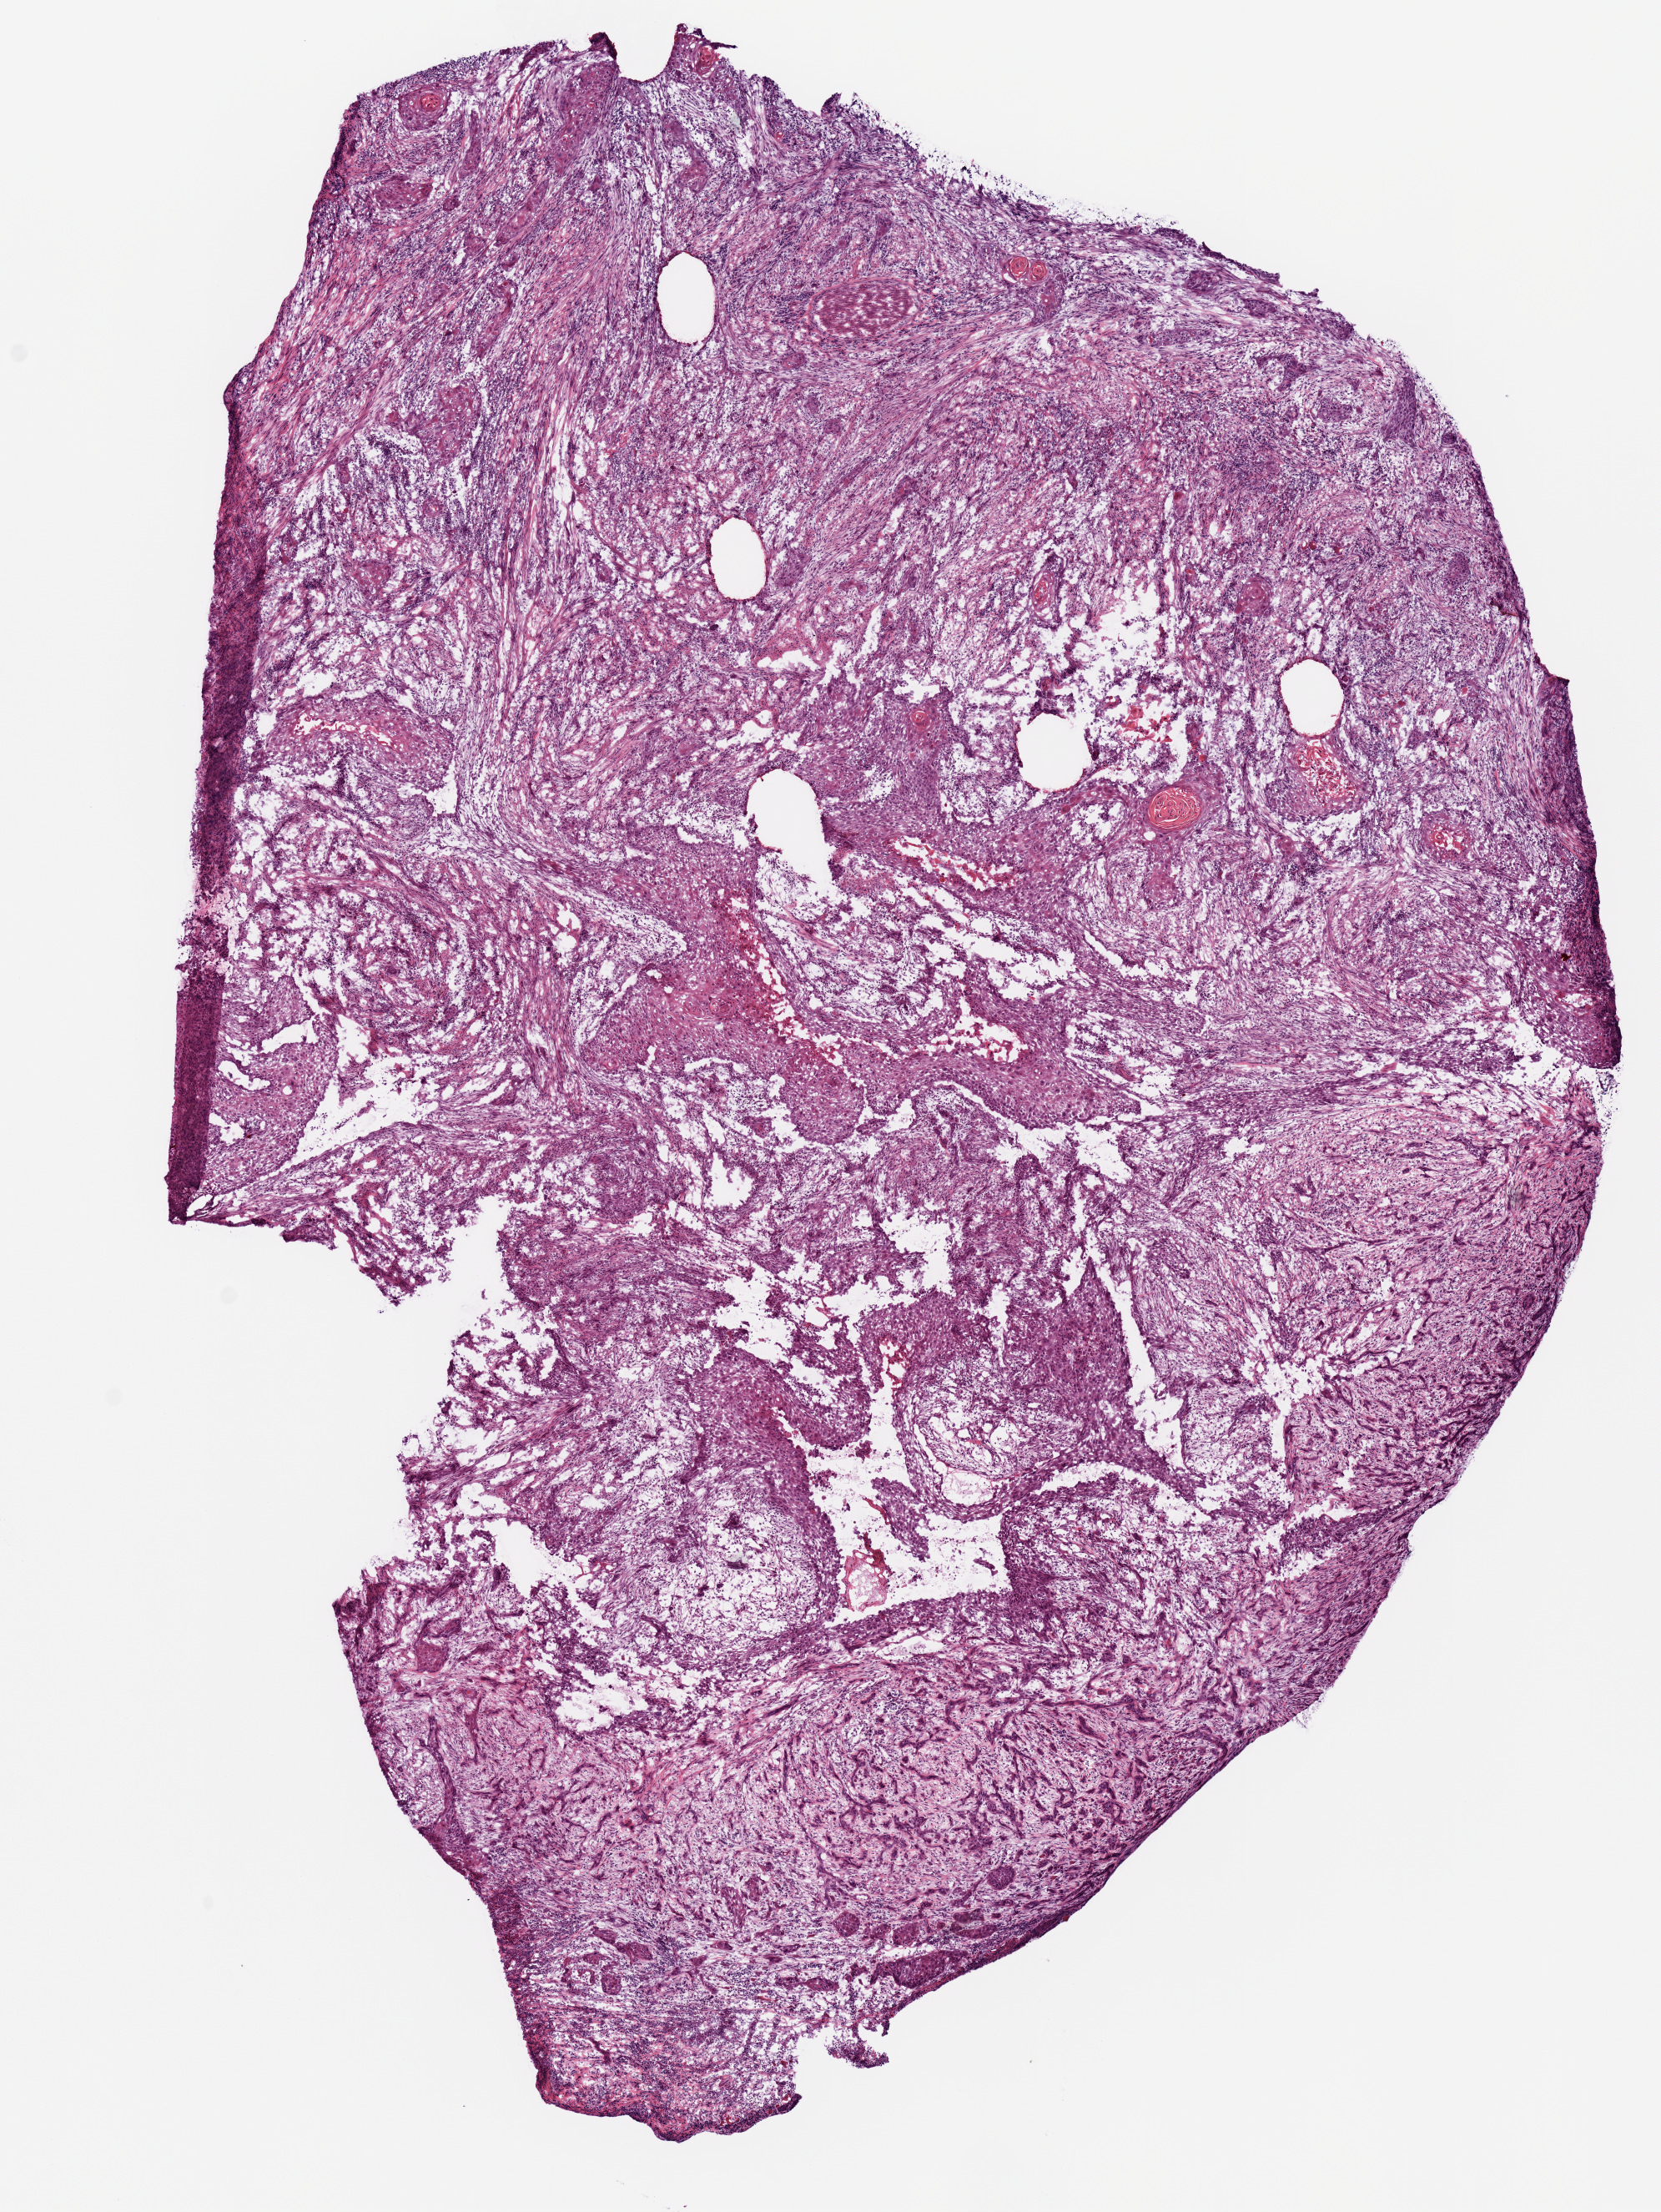
Whole-slide histology image, H&E, shown as a low-resolution overview of the whole scanned area (about 7.9 x 10.5 mm), frozen section, sample: primary tumour, head and neck. Male patient; age at initial diagnosis 74 years. Histologic grade: G2 (moderately differentiated). Slide review estimates, as recorded: tumour cells 75%, tumour nuclei 60%, normal cells 60%, stromal cells 25%, necrosis 0%.
AJCC pathologic stage: IVA (7th edition). Histologic diagnosis: Squamous cell carcinoma, NOS (tongue, NOS).